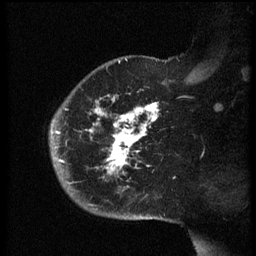
Breast MRI (dynamic contrast-enhanced), one sagittal slice. Slice 46 of 60 in the series (ordered by position). Dynamic contrast-enhanced series, image 2 of 3 at this slice position (ordered by acquisition). 1.5 T. TE 4.2 ms, TR 8.4 ms. 2.5 mm slice thickness. 256 × 256 image matrix, field of view 200 × 200 mm. Patient: female, 38 years. Case-level facts recorded for this patient, not image findings: setting: breast cancer imaged before/during neoadjuvant chemotherapy; receptor status: HER2-positive.
Outlined on this slice (semi-automatically segmented with operator editing):
- analysis volume of interest (the breast-tissue region the enhancement analysis was run in; not a lesion): bounding box (x1, y1, x2, y2) in pixels: (50, 74, 169, 202)
- tumour enhancement mask (voxels above the 70 % enhancement threshold inside the analysis volume of interest): (52, 95, 159, 175)